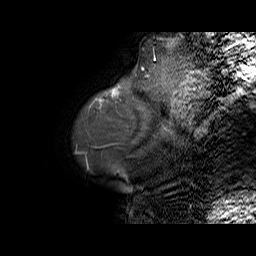
Breast MRI (dynamic contrast-enhanced), one sagittal slice. Position 7 of 70 along the scan axis. Dynamic contrast-enhanced series, time point 2 of 6 at this slice position (early post-contrast). 1.5 T. TE 5.5 ms, TR 32.9 ms. 4 mm slice thickness. 256 × 256 image matrix. Female patient. Case-level facts recorded for this patient, not image findings: setting: breast cancer imaged before/during neoadjuvant chemotherapy; receptor status: HER2-positive.
Outlined on this slice (semi-automatically segmented with operator editing):
- analysis volume of interest (the breast-tissue region the enhancement analysis was run in; not a lesion): box from (x=96, y=81) to (x=141, y=110) px
- tumour enhancement mask (voxels above the 100 % enhancement threshold inside the analysis volume of interest): (x=100, y=88)–(x=119, y=102)